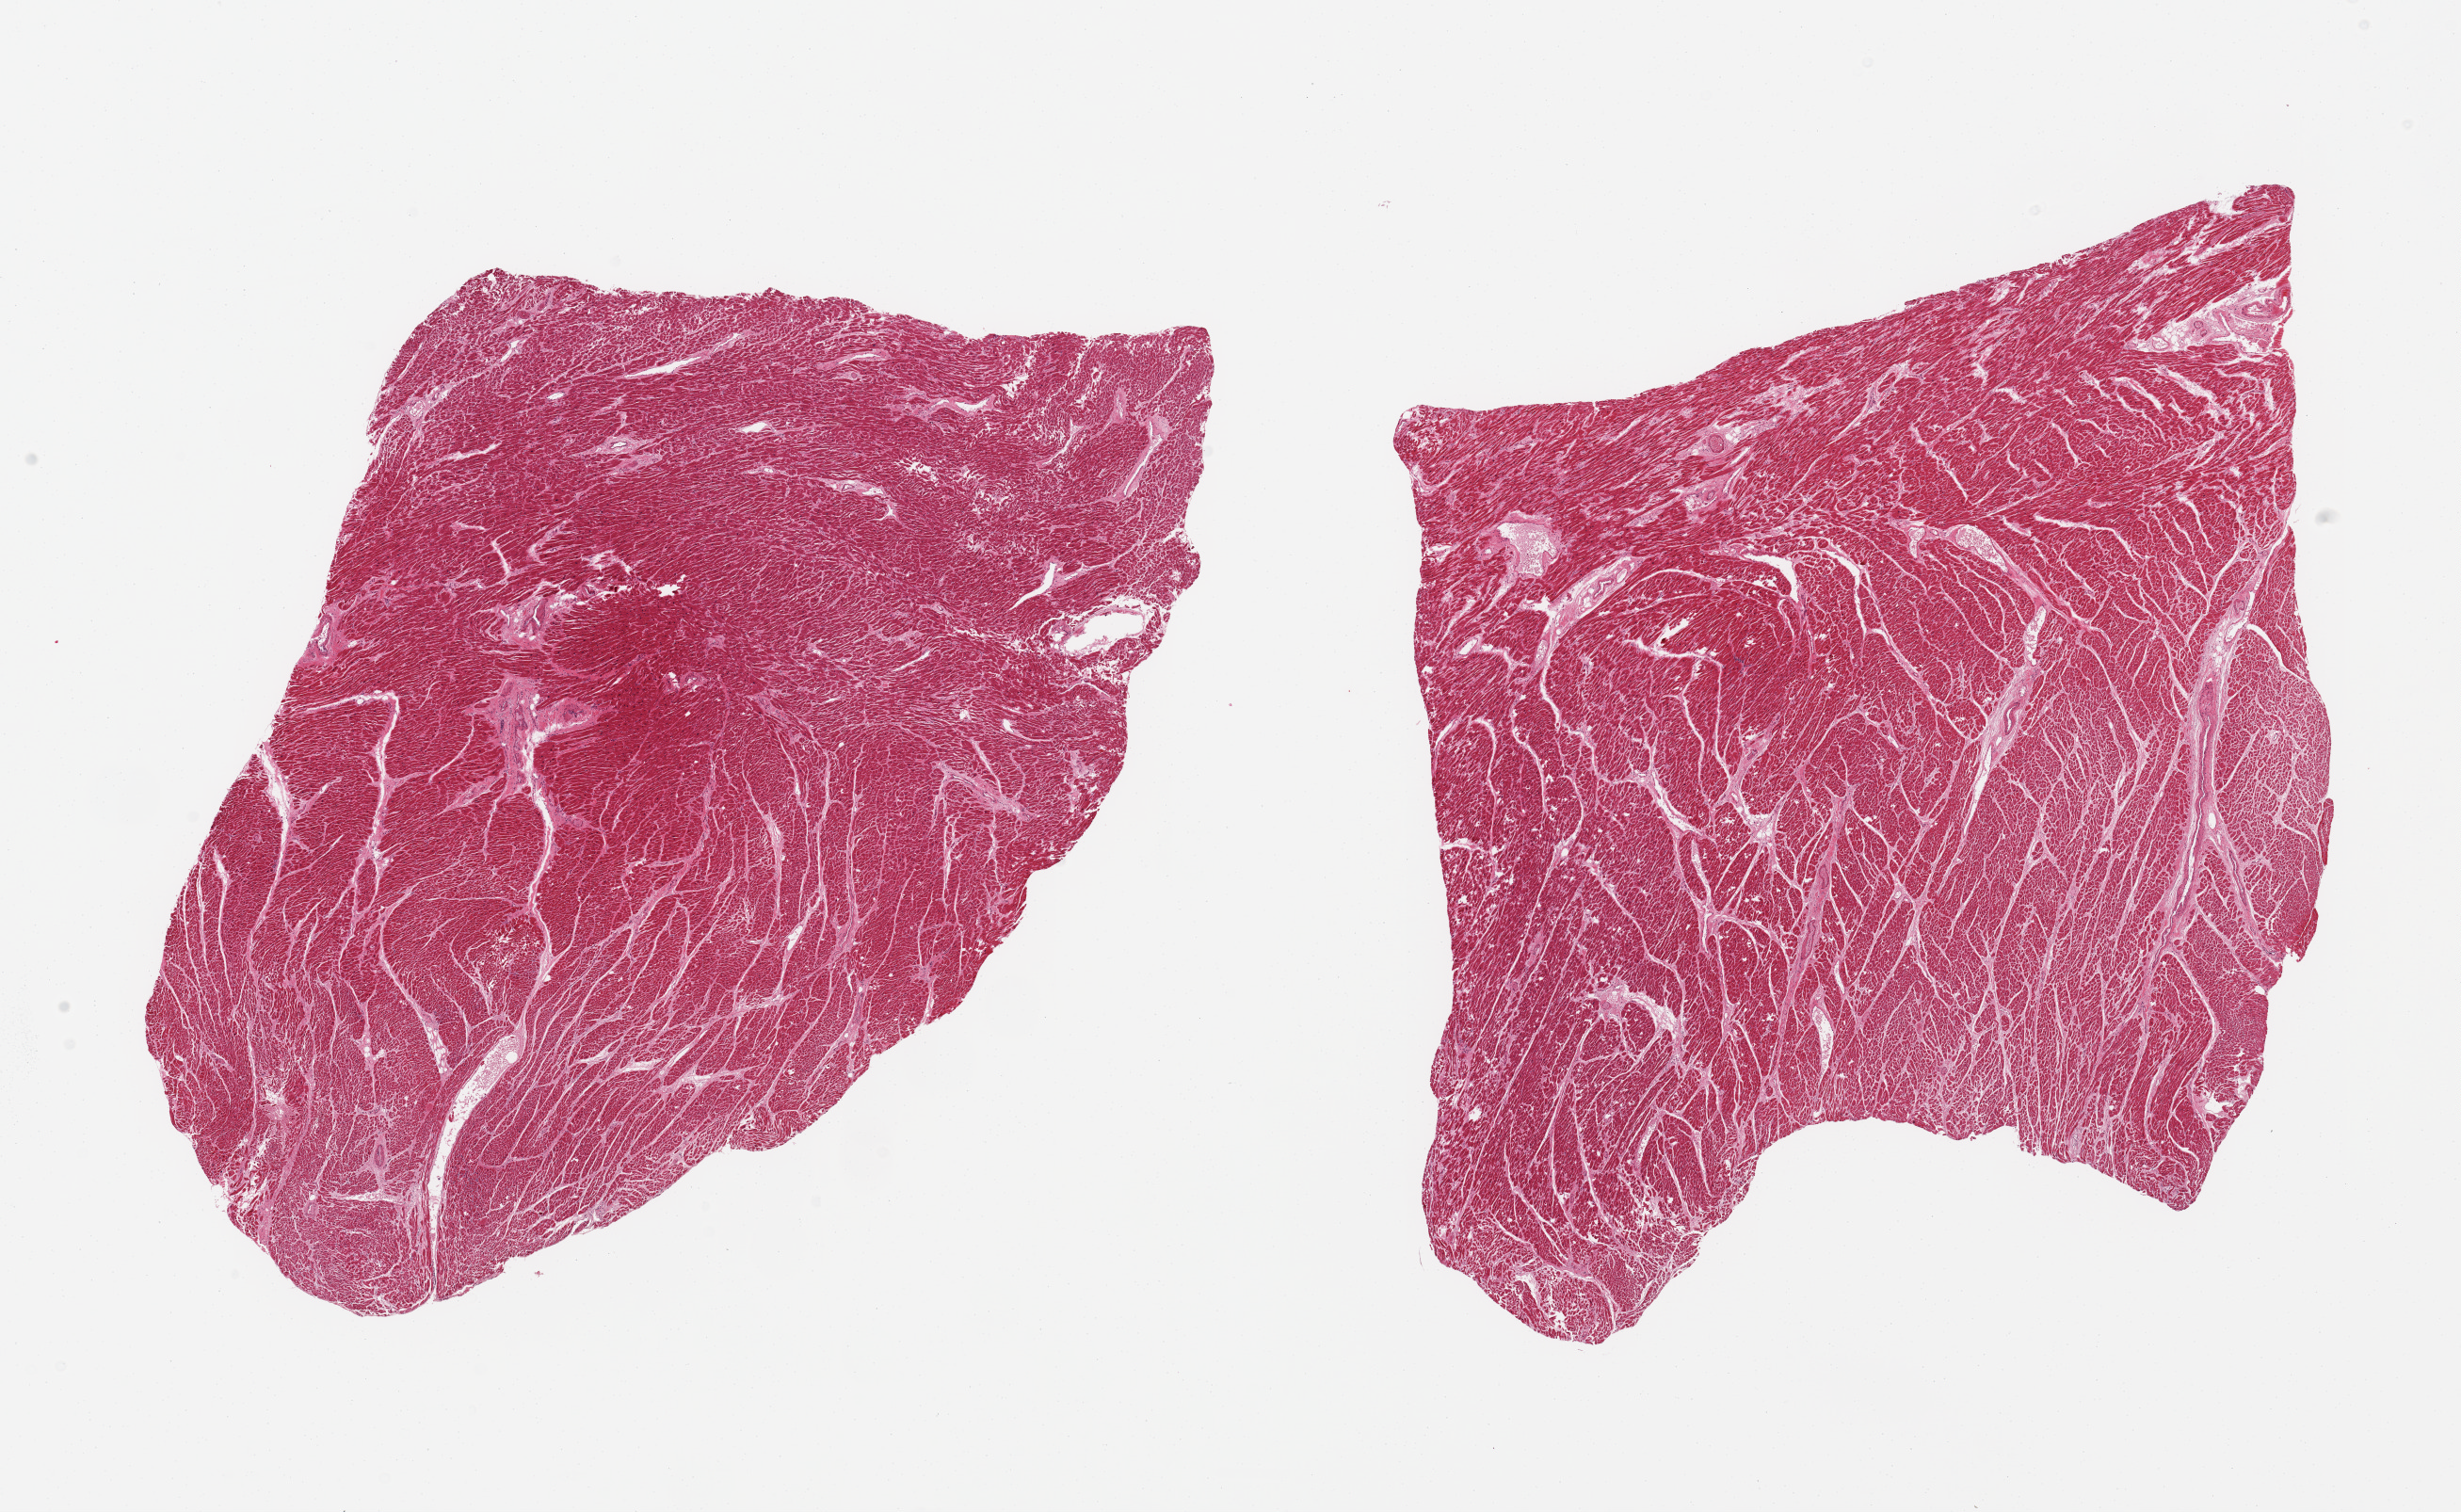
Digitized haematoxylin and eosin-stained section, whole scanned area (about 20.7 x 12.7 mm) shown as a low-resolution overview. PAXgene-fixed, paraffin-embedded tissue. Section of heart (target tissue). Donor tissue sample. Donor sex: male.
- pathologist's review note for this sample: 2 pieces; focal hypereosinophilia, but no obvious infarction